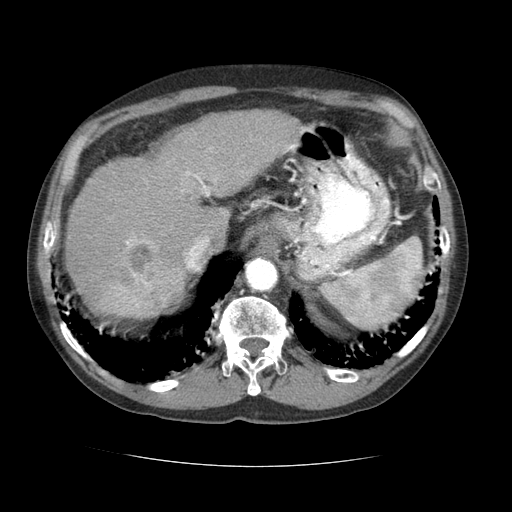
Contrast-enhanced abdominal CT (liver protocol), one axial slice; position 51 of 69 along the scan axis; soft-tissue window (W 400 / L 40 HU); 2.5 mm slice thickness; 512 × 512 image matrix, field of view 360 × 360 mm. From the clinical record (not read from this slice): diagnosis: hepatocellular carcinoma (patient treated with transarterial chemoembolisation; whether this scan precedes or follows treatment is not stated here); TNM stage (as recorded): Stage-II.
Outlined on this slice (semi-automatically segmented with operator editing):
- liver parenchyma outside the tumour (the mass and vessels are separate outlines, so this box may not span the whole liver): box from (x=64, y=110) to (x=304, y=318) px
- mass: (x=87, y=237)–(x=183, y=317)
- liver vessels: (x=185, y=144)–(x=296, y=268)